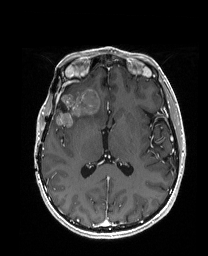
Brain MRI from a brain-tumour surgery series, one axial slice; position 89 of 192 along the scan axis; T1-weighted post-contrast; 1 mm slice thickness; 208 × 256 image matrix, field of view 203 × 250 mm. From the clinical record (not read from this slice): histopathology: Metastatic Carcinoma from Breast primary; tumour location: Right Frontal.
Outlined on this slice (manually delineated by an expert):
- previous resection cavity: bounding box <57,86,68,112> (left, top, right, bottom; pixels)
- tumour: <55,87,104,126>